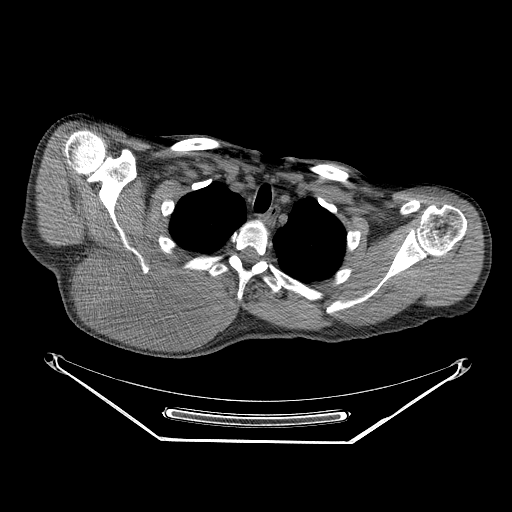
CT of an extremity soft-tissue mass (from a PET/CT study), one axial slice. Slice 199 of 267 in the series (ordered by position). Reconstruction kernel STANDARD. 140 kVp. Soft-tissue window (W 400 / L 40 HU). 512 × 512 image matrix, field of view 500 × 500 mm. Male patient. Case-level facts recorded for this patient, not image findings: histological type: pleiomorphic spindle cell undifferentiated; grade: high; site of the primary tumour: right parascapusular.
Outlined on this slice (expert contour drawn on MRI and transferred to this co-registered scan by the dataset authors):
- gross tumour volume including surrounding oedema: box from (x=77, y=251) to (x=236, y=336) px
- gross tumour volume (mass): (x=77, y=253)–(x=220, y=334)